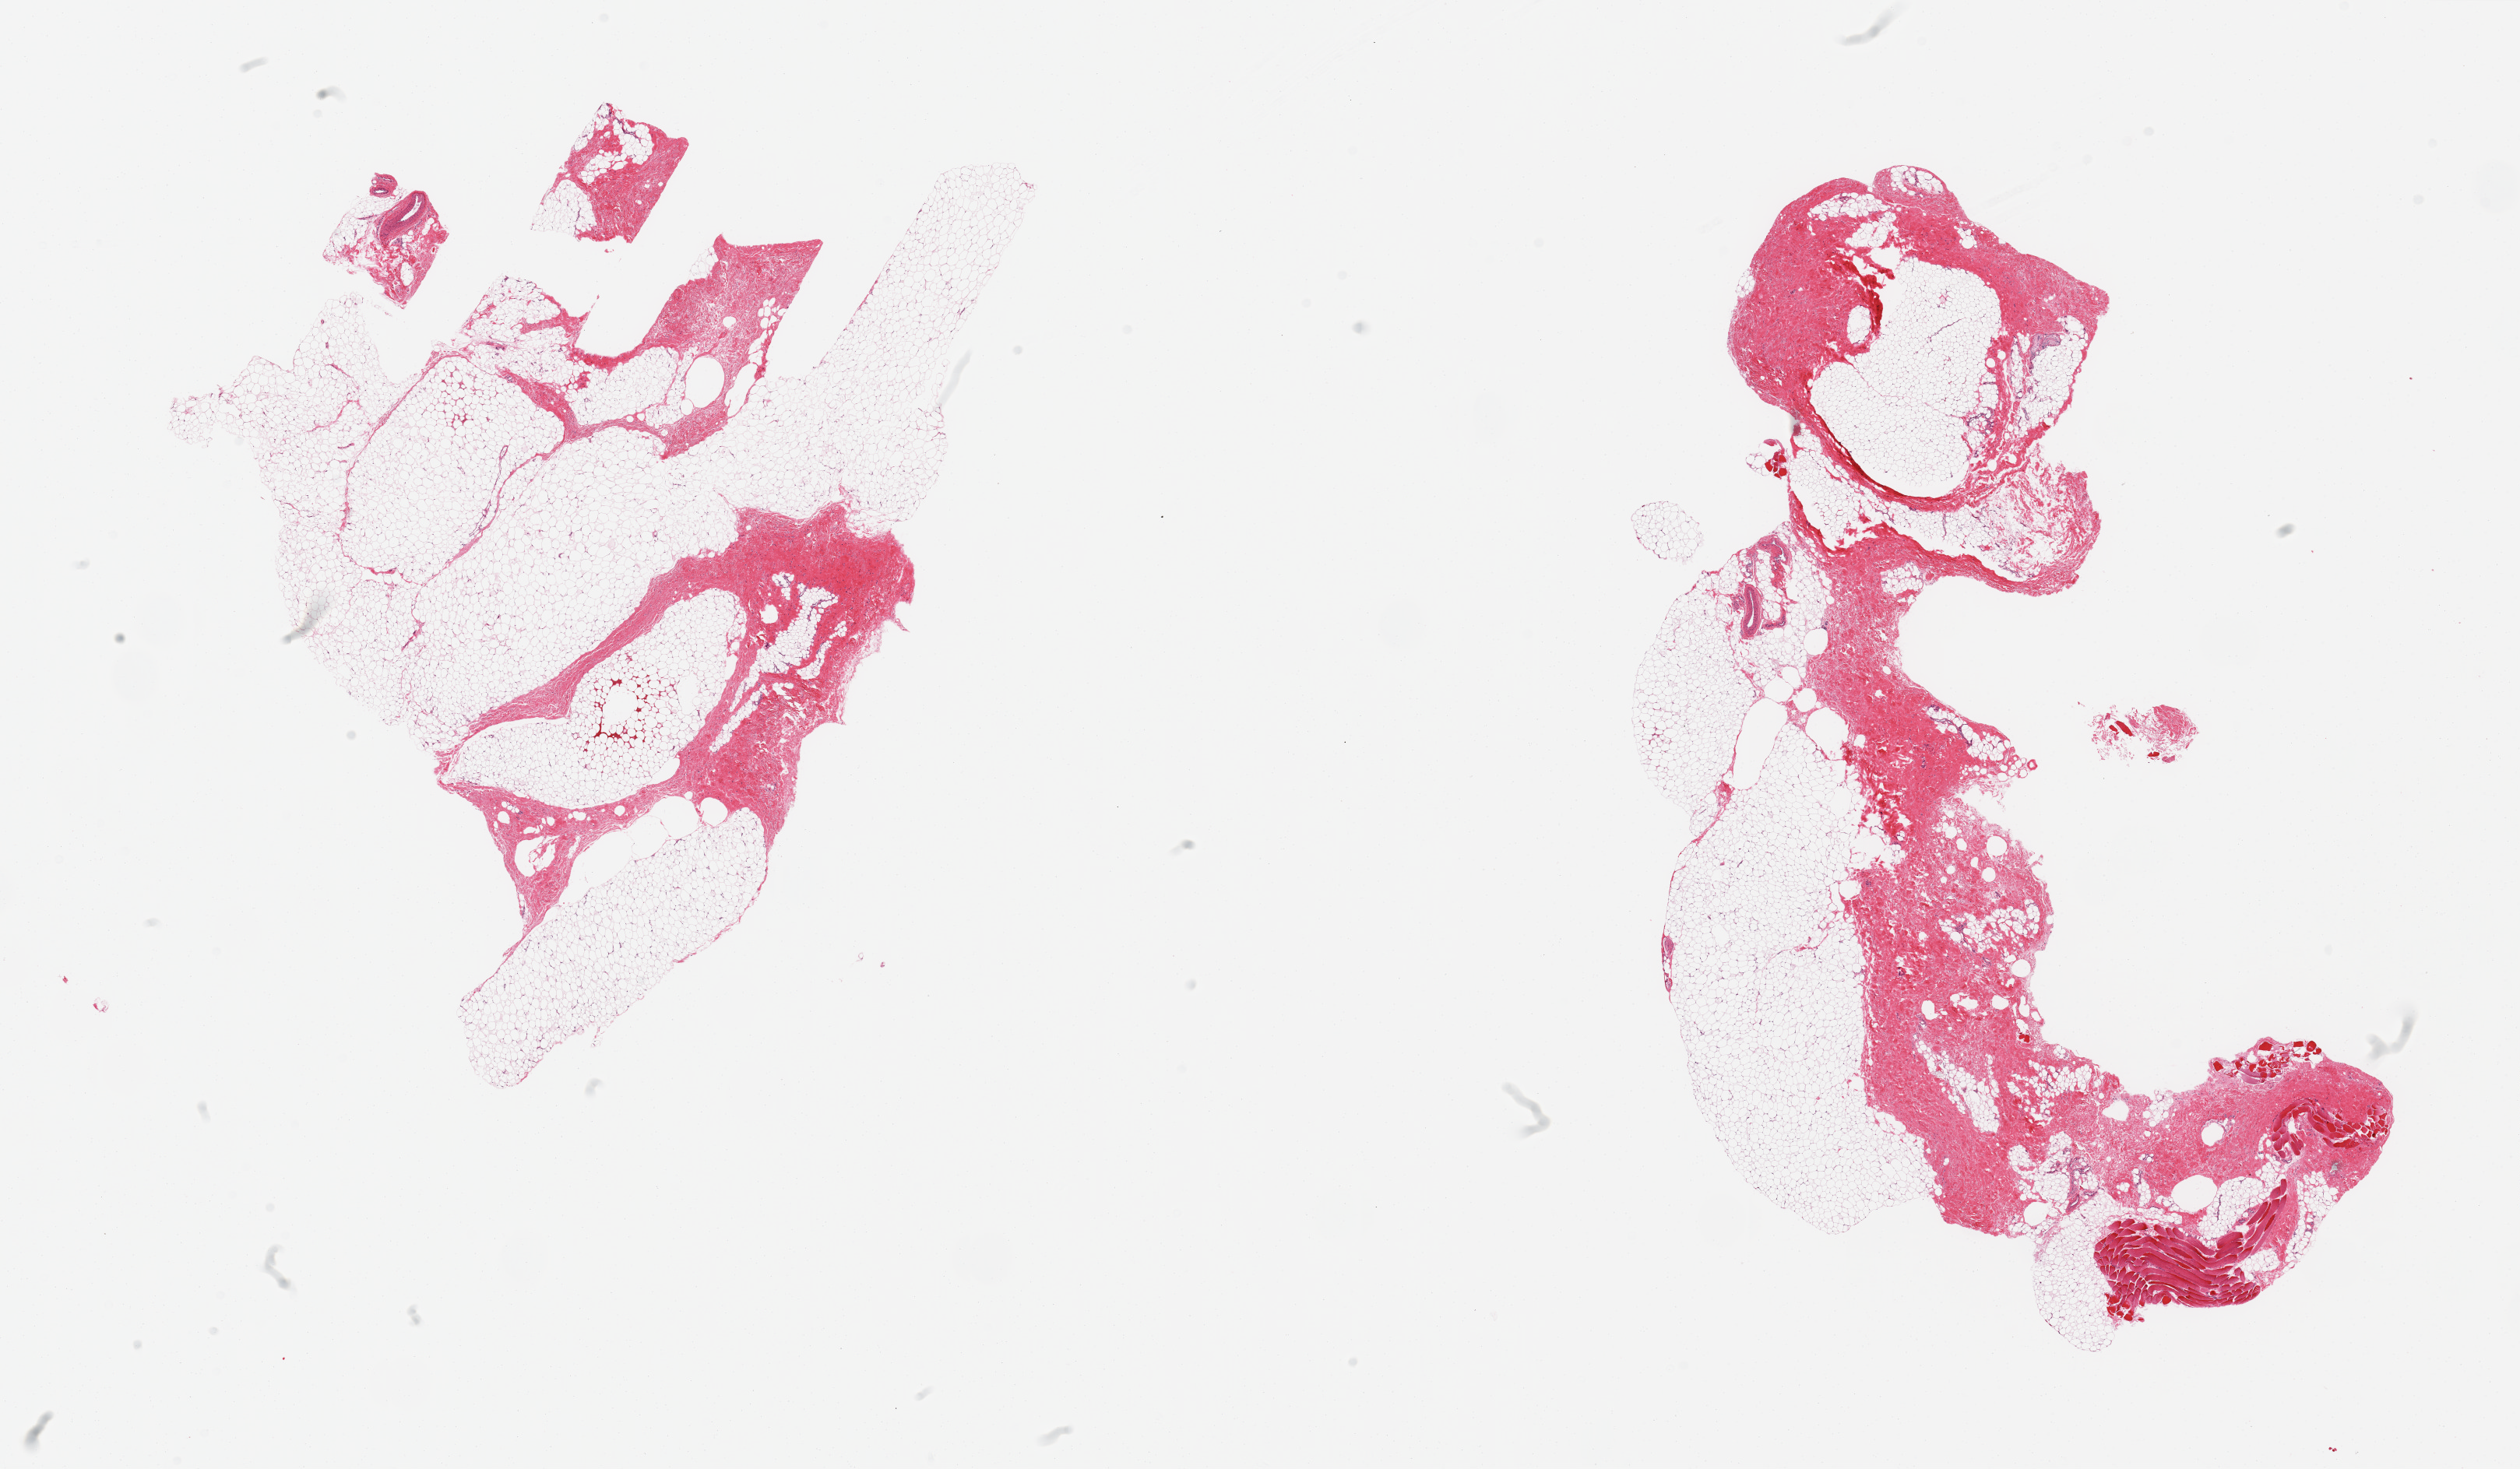
Digitized H&E-stained section, a low-resolution overview of the entire scanned area, about 25.6 x 14.9 mm (from a 20x scan). PAXgene-fixed, paraffin-embedded tissue. Section of breast (target tissue). Tissue donor sample.
• pathologist's review note for this sample: 2 pieces, fibroadipose tissues/stroma; no ductal elements